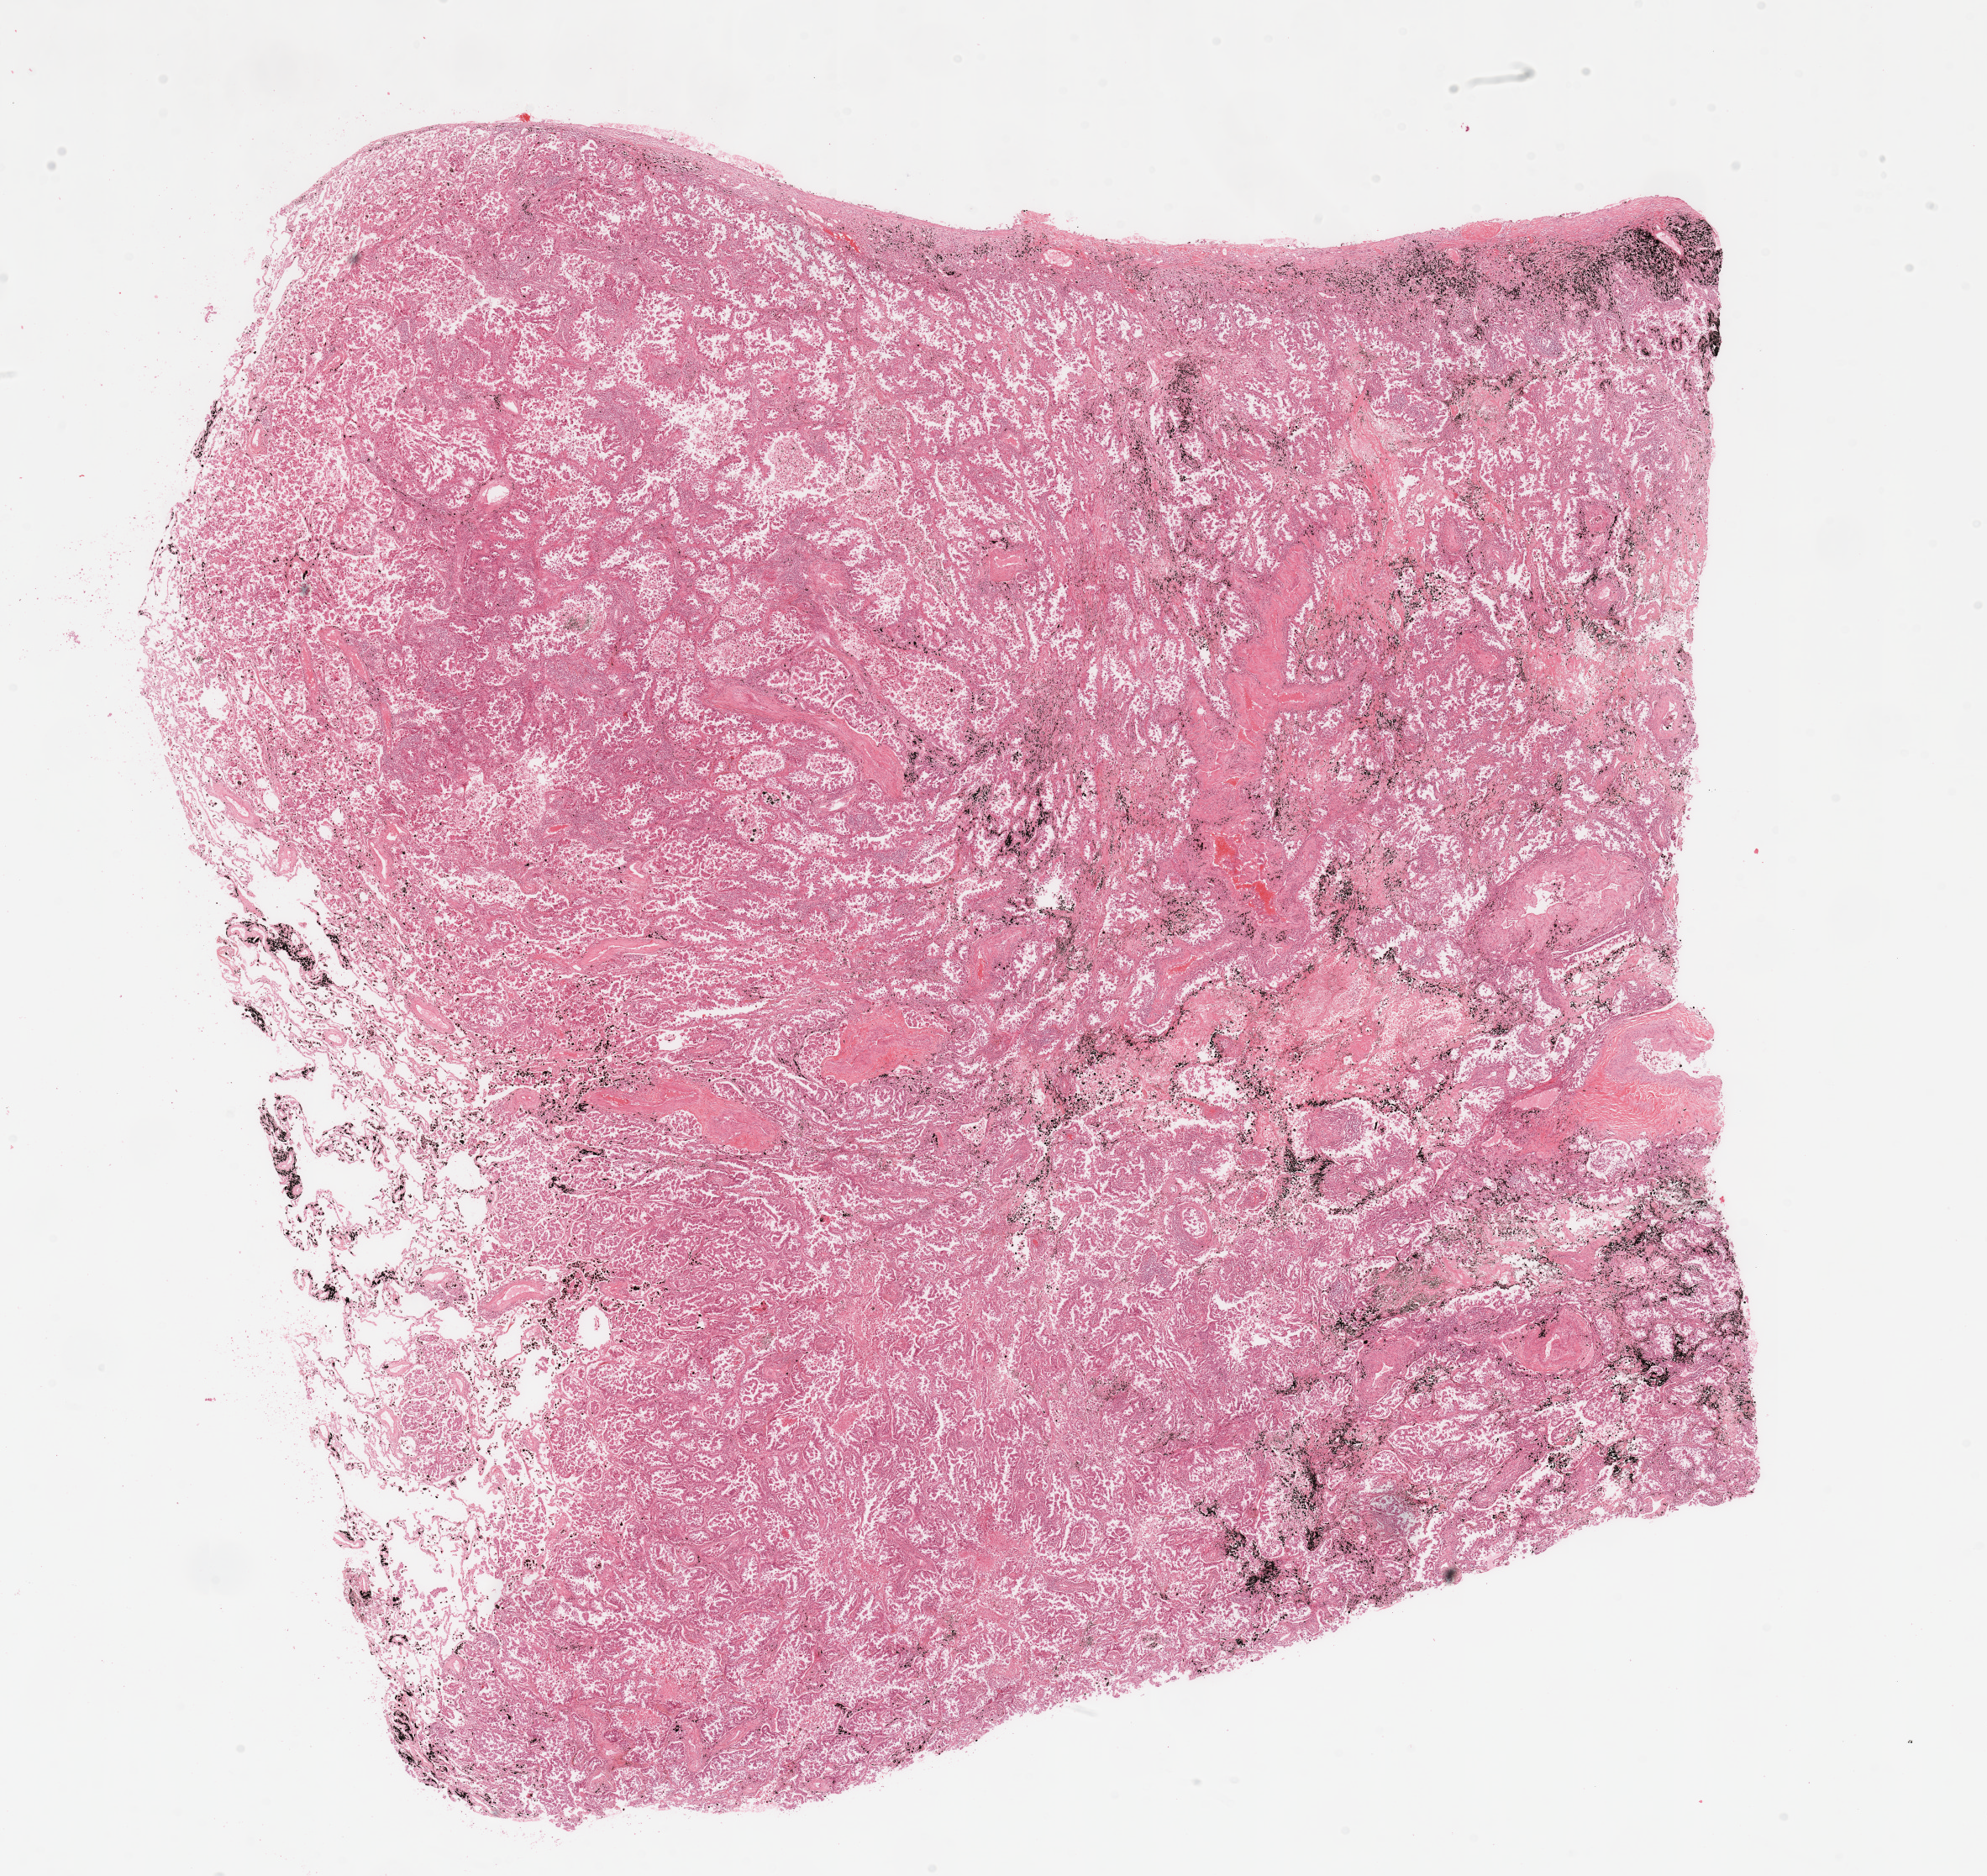
Hematoxylin and eosin (H&E) stained whole-slide image — shown as a low-resolution overview of the whole scanned area (about 18.7 x 17.7 mm, from a 20x scan). Tumour tissue sample, lung. 72-year-old male patient. Histologic grade: G2 (moderately differentiated).
AJCC pathologic stage: IB. Diagnosis: Adenocarcinoma, NOS.